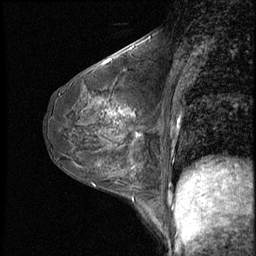
Breast MRI (dynamic contrast-enhanced), one sagittal slice; slice 29 of 50 in the series (ordered by position); 3 images stored at this slice position (order not interpretable as contrast timing); 1.5 T; TE 4.2 ms, TR 8.7 ms; 2.5 mm slice thickness; 256 × 256 image matrix, field of view 180 × 180 mm. Patient: female, 43 years. Case-level facts recorded for this patient, not image findings: setting: breast cancer imaged before/during neoadjuvant chemotherapy; receptor status: HR-positive, HER2-negative.
Annotated regions visible in this slice (semi-automatically segmented with operator editing):
- analysis volume of interest (the breast-tissue region the enhancement analysis was run in; not a lesion): bounding box (x1, y1, x2, y2) in pixels: (122, 109, 159, 155)
- tumour enhancement mask (voxels above the 140 % enhancement threshold inside the analysis volume of interest): (122, 110, 143, 140)